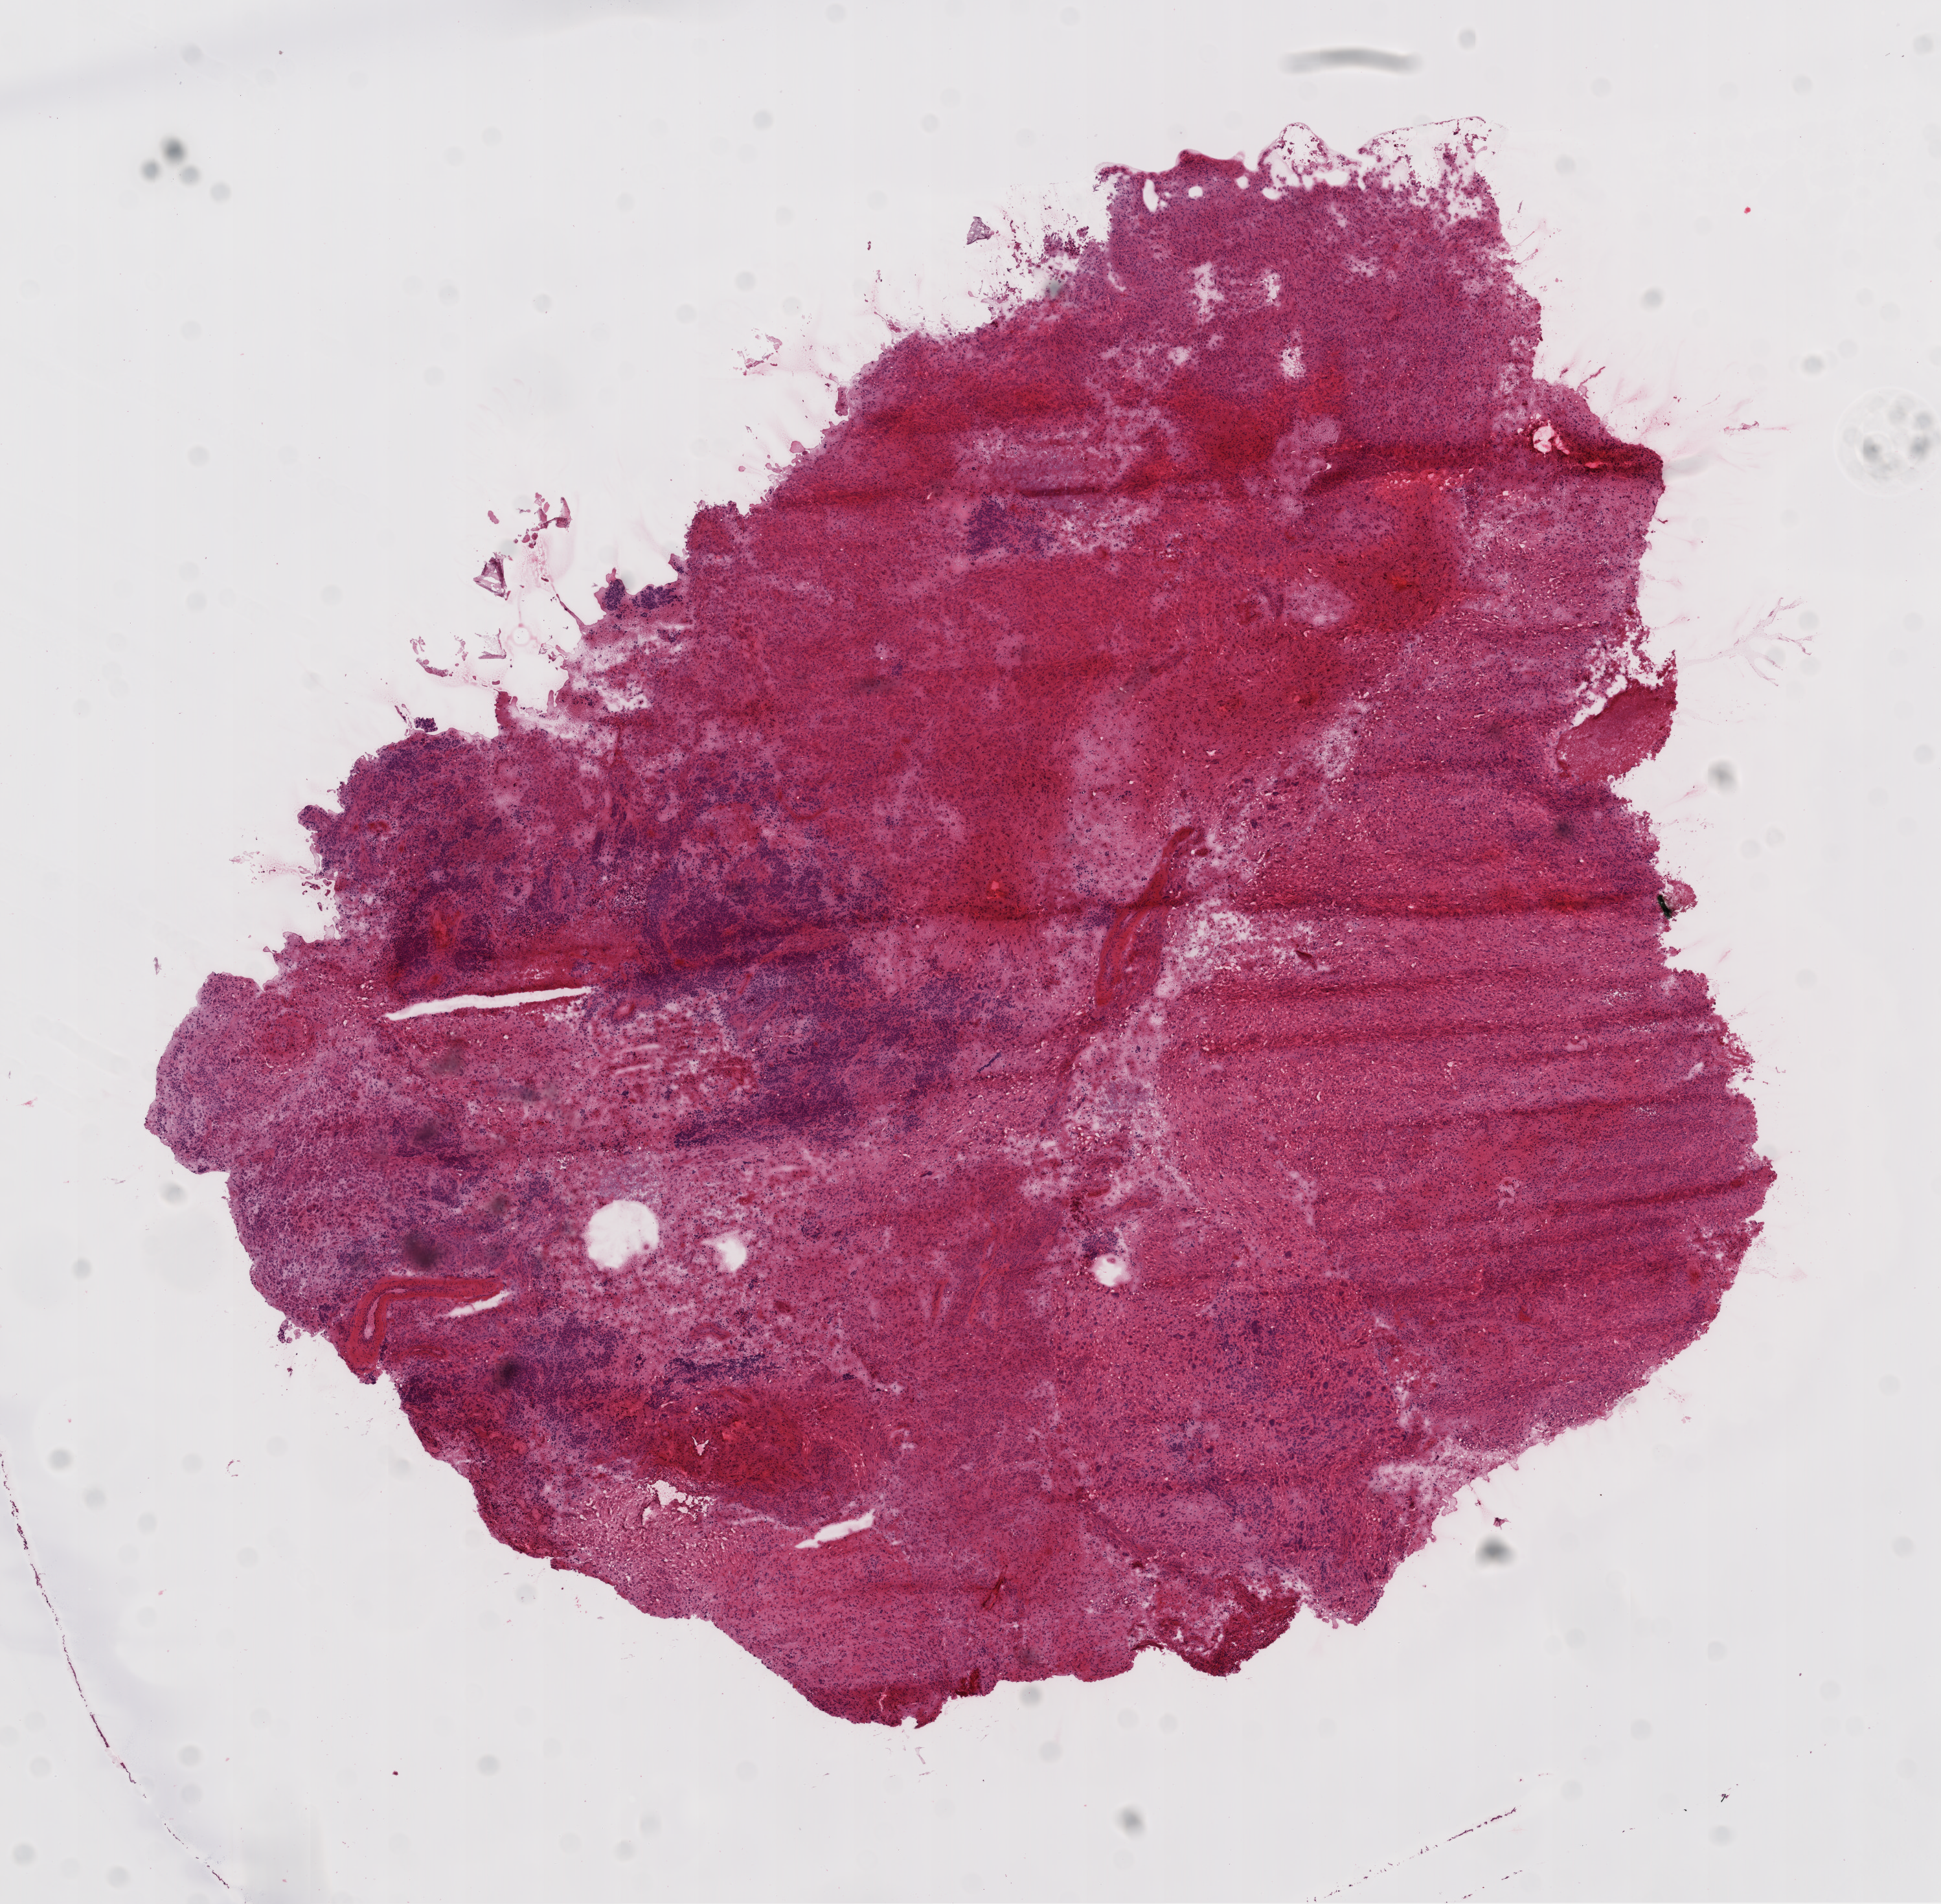
Whole-slide histology image, Hematoxylin and eosin (H&E) stained, whole scanned area (about 12.1 x 11.9 mm, acquisition: 20x scan) shown as a low-resolution overview; frozen section from the top of the tissue portion; sample: primary tumour, brain. Patient: male, age at initial diagnosis 60 years. Composition of this section per pathologist review: tumour cells 95%, tumour nuclei 100%, normal cells 0%, stromal cells 0%, necrosis 5%.
• pathologic diagnosis: Glioblastoma